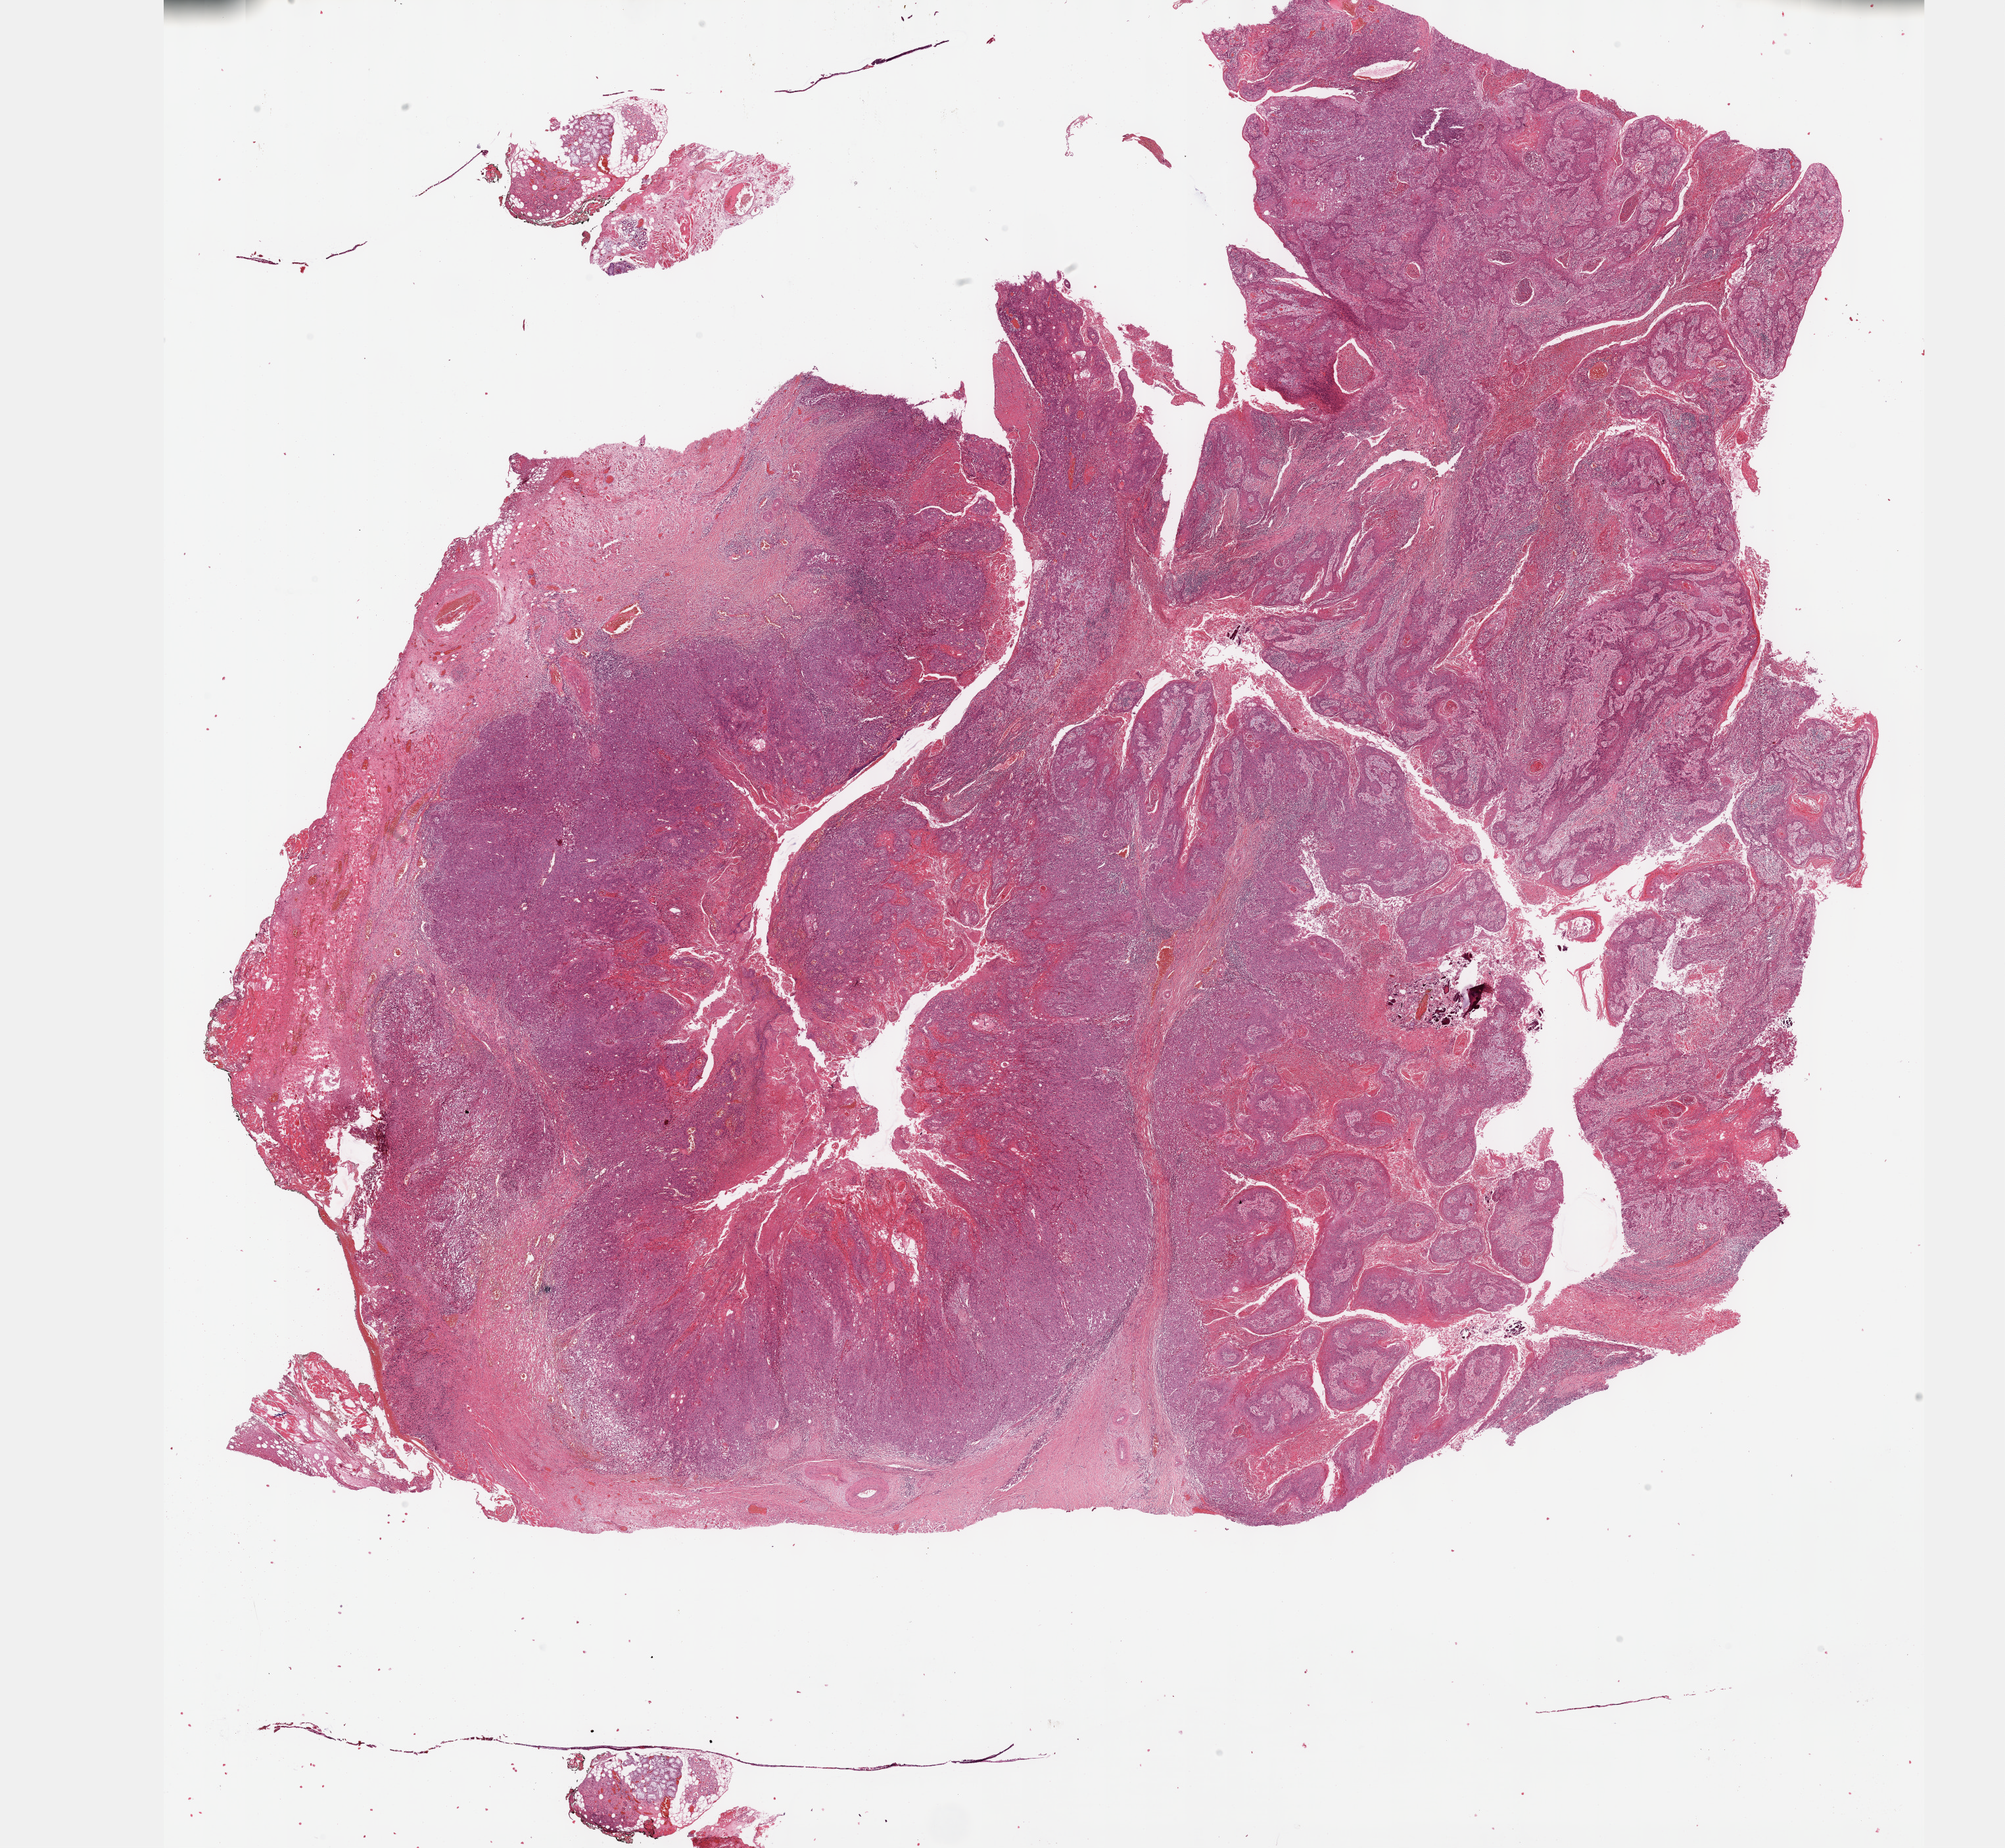
H&E-stained whole-slide image — whole scanned area (about 24.6 x 22.7 mm, from a 40x scan) shown as a low-resolution overview, formalin-fixed paraffin-embedded (FFPE) diagnostic section, head and neck, primary tumour sample. Female patient; age at initial diagnosis 72 years. Histologic grade: G3 (poorly differentiated).
* pathologic diagnosis: Squamous cell carcinoma, NOS (floor of mouth, NOS)
* laterality: right
* AJCC pathologic stage: IVA (6th edition)